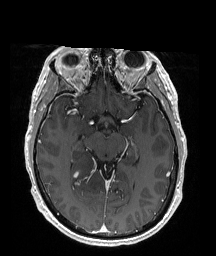
Brain MRI from a brain-tumour surgery series, one axial slice. Position 108 of 176 along the scan axis. T1-weighted post-contrast. 1 mm slice thickness. 216 × 256 image matrix, field of view 211 × 250 mm. Case-level facts recorded for this patient, not image findings: histopathology: Oligodendroglioma; WHO grade: 2.
Outlined on this slice (manually delineated by an expert):
- tumour: box from (x=70, y=150) to (x=111, y=205) px